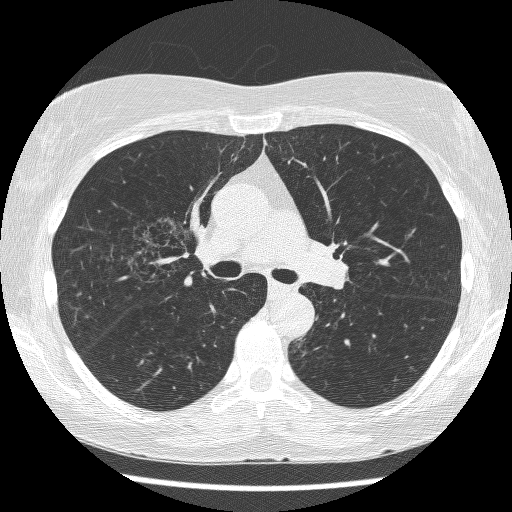
Axial slice from a low-dose chest CT screening exam. First (baseline) screen. Lung window (W 1500 / L -600 HU). 1.25 mm slice thickness. Slice 172 of 271 in the series. Female, age 64 years at enrolment. Former smoker at enrolment.
• Expert-annotated lung lesion, bounding box <124,219,202,286> (left, top, right, bottom; pixels).
• The screening reader recorded 3 non-calcified nodules or masses ≥4 mm on this exam (right upper lobe, right upper lobe, left lower lobe); which of them this box marks is not recorded.
• Later outcome: lung cancer diagnosed 735 days after this screen — adenocarcinoma, NOS, right upper lobe, right middle lobe, right hilum, stage IV (AJCC 6th edition), 85 mm at pathology.